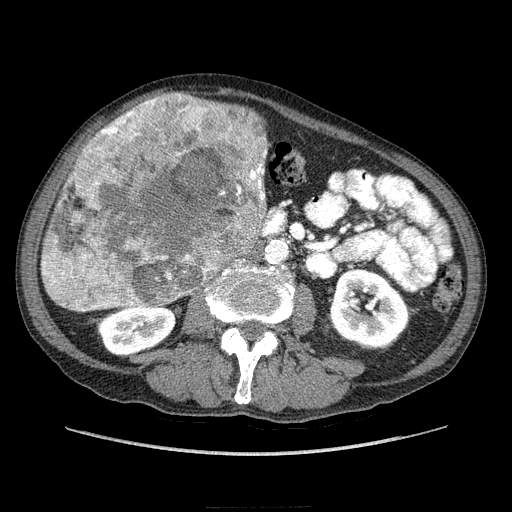
Contrast-enhanced abdominal CT (liver protocol), one axial slice; position 77 of 218 along the scan axis; reconstruction kernel STANDARD; 100 kVp; soft-tissue window (W 400 / L 40 HU); 512 × 512 image matrix, field of view 380 × 380 mm. Case-level facts recorded for this patient, not image findings: diagnosis: hepatocellular carcinoma (patient treated with transarterial chemoembolisation; whether this scan precedes or follows treatment is not stated here); TNM stage (as recorded): Stage-IIIA; Child-Pugh class: A.
Structures marked on this image (semi-automatically segmented with operator editing):
- liver parenchyma outside the tumour (the mass and vessels are separate outlines, so this box may not span the whole liver): bounding box <40,132,266,312> (left, top, right, bottom; pixels)
- mass: <42,93,269,311>